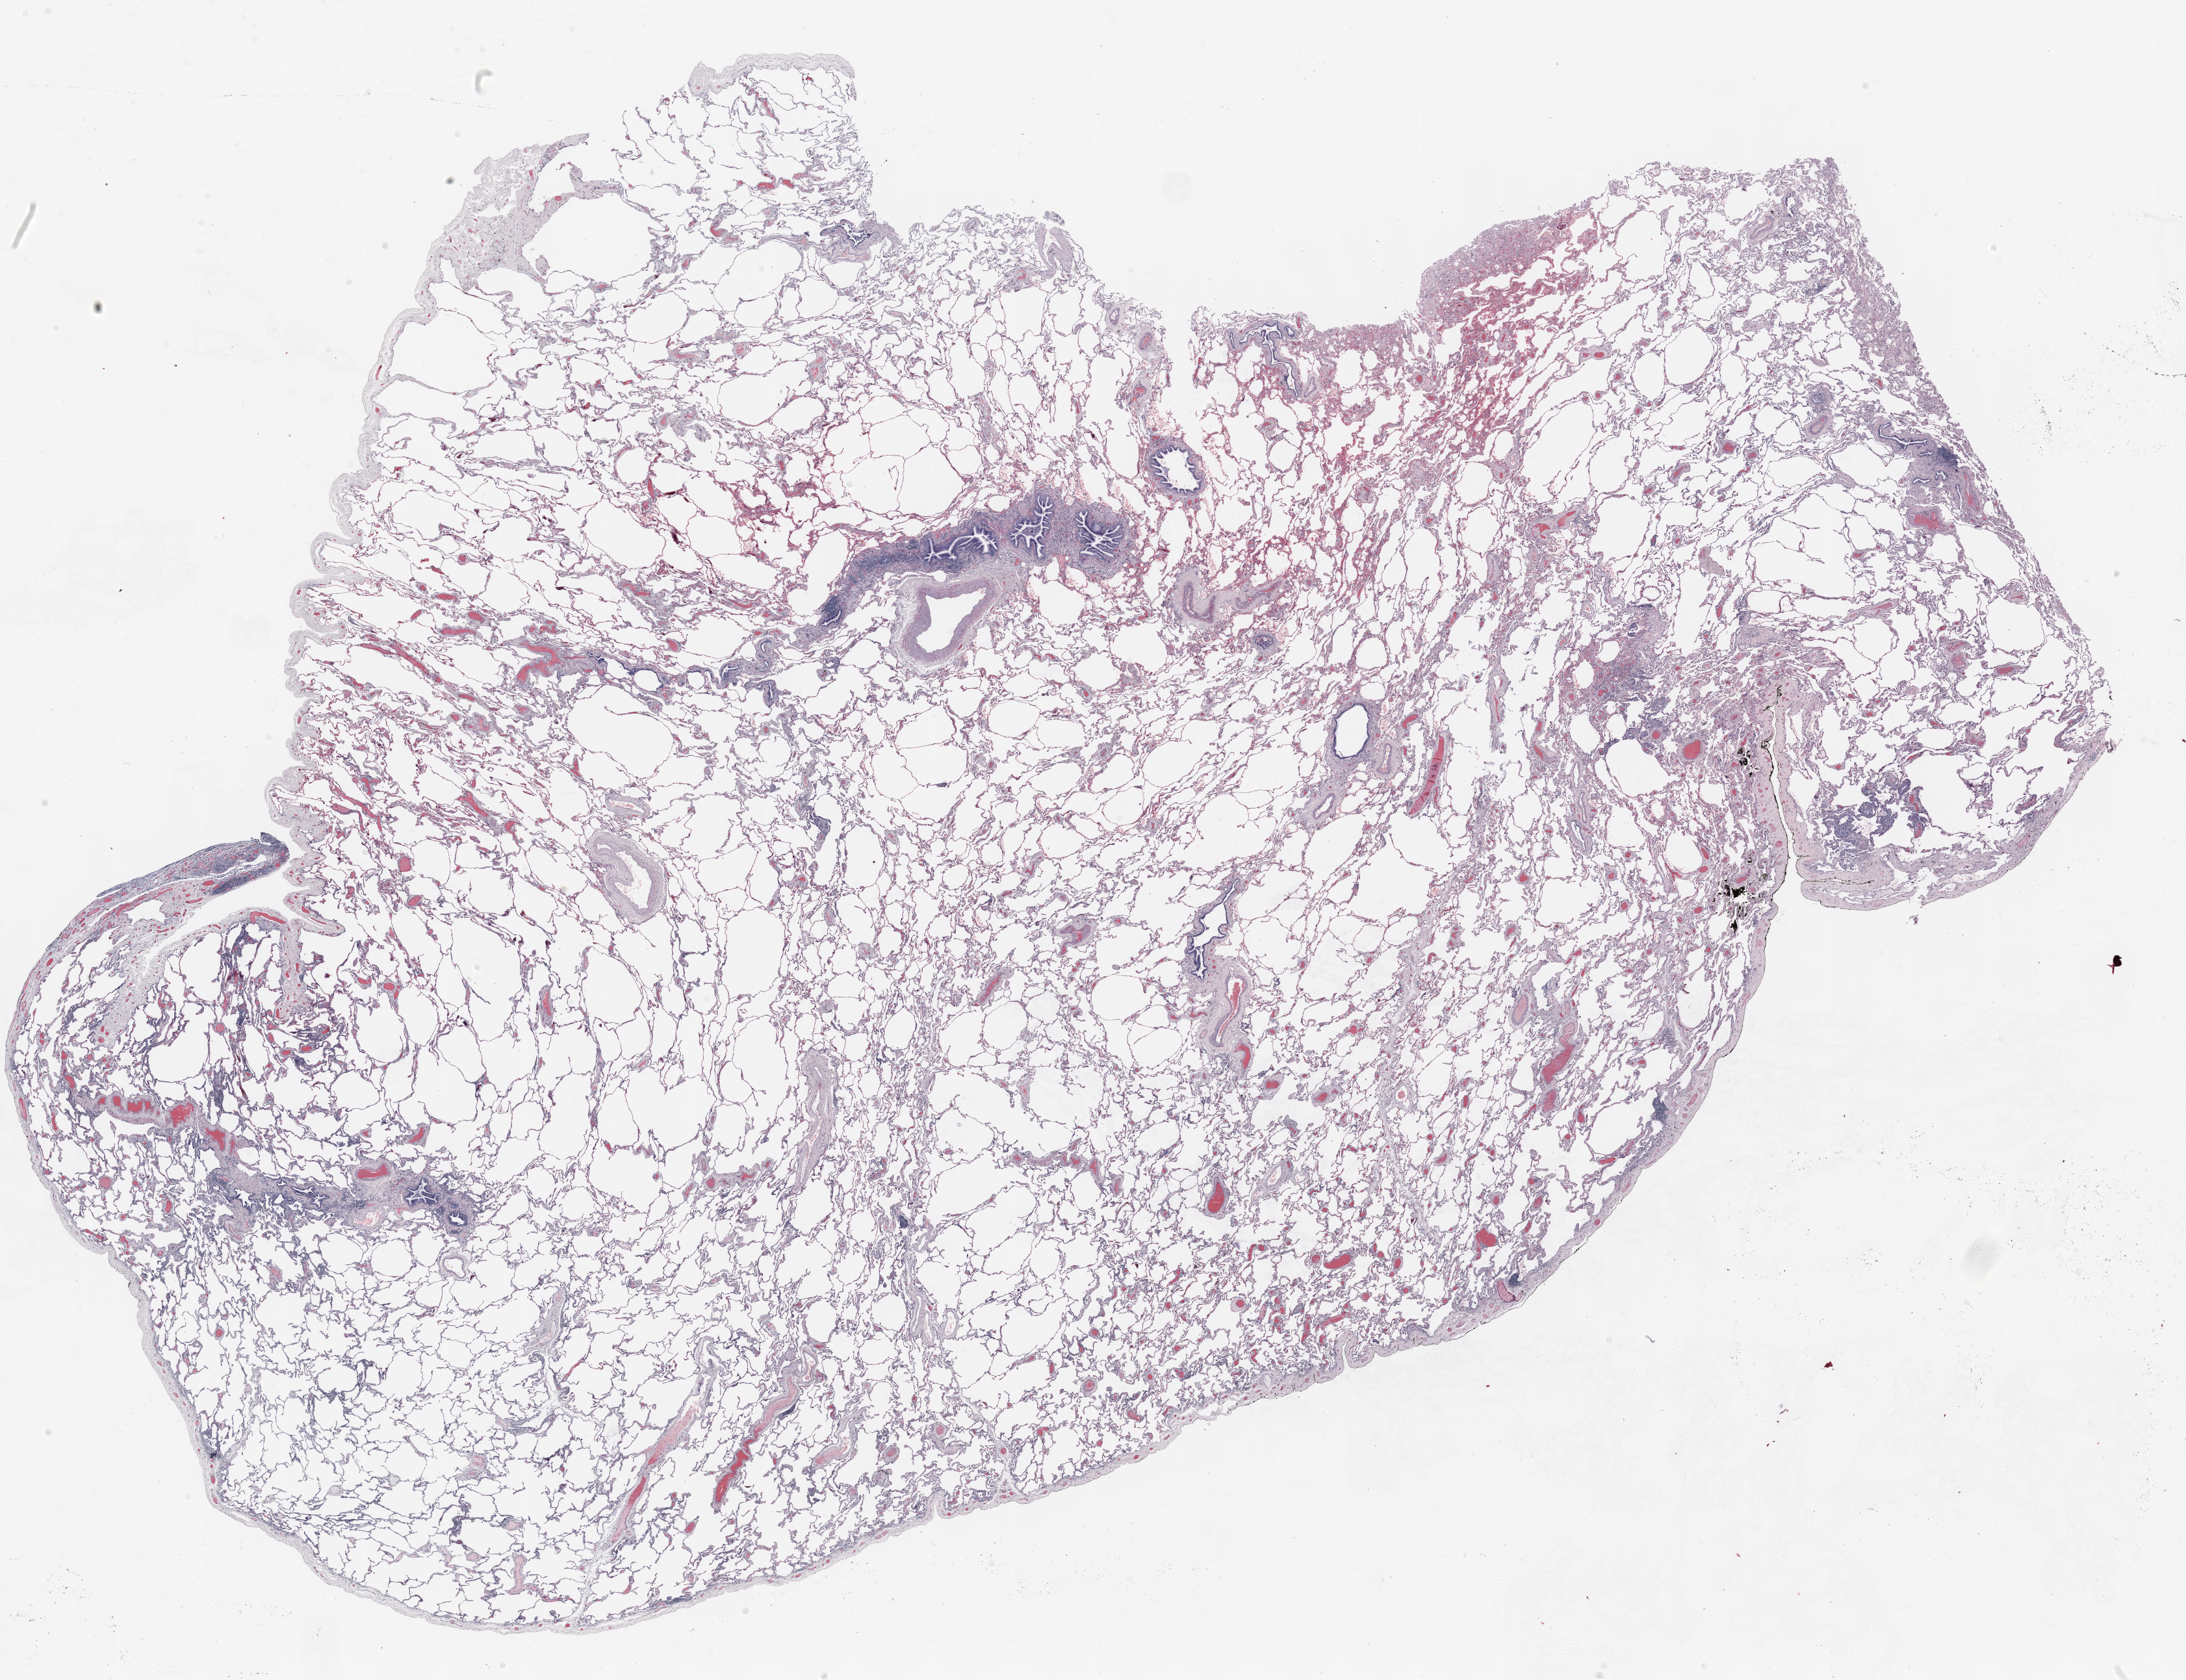
Hematoxylin and eosin (H&E) stained whole-slide image, whole scanned area (about 27.0 x 20.8 mm) shown as a low-resolution overview, formalin-fixed paraffin-embedded (FFPE) section, lung tissue. Female, age 66 at enrolment. Former smoker at enrolment. Grade: moderately differentiated (G2).
Primary tumour location (clinical record): right middle lobe. Participant's lung-cancer diagnosis: Adenocarcinoma, NOS (ICD-O-3 8140/3). Stage (AJCC 6th edition): IA. Tumour size (pathology): 11 mm.